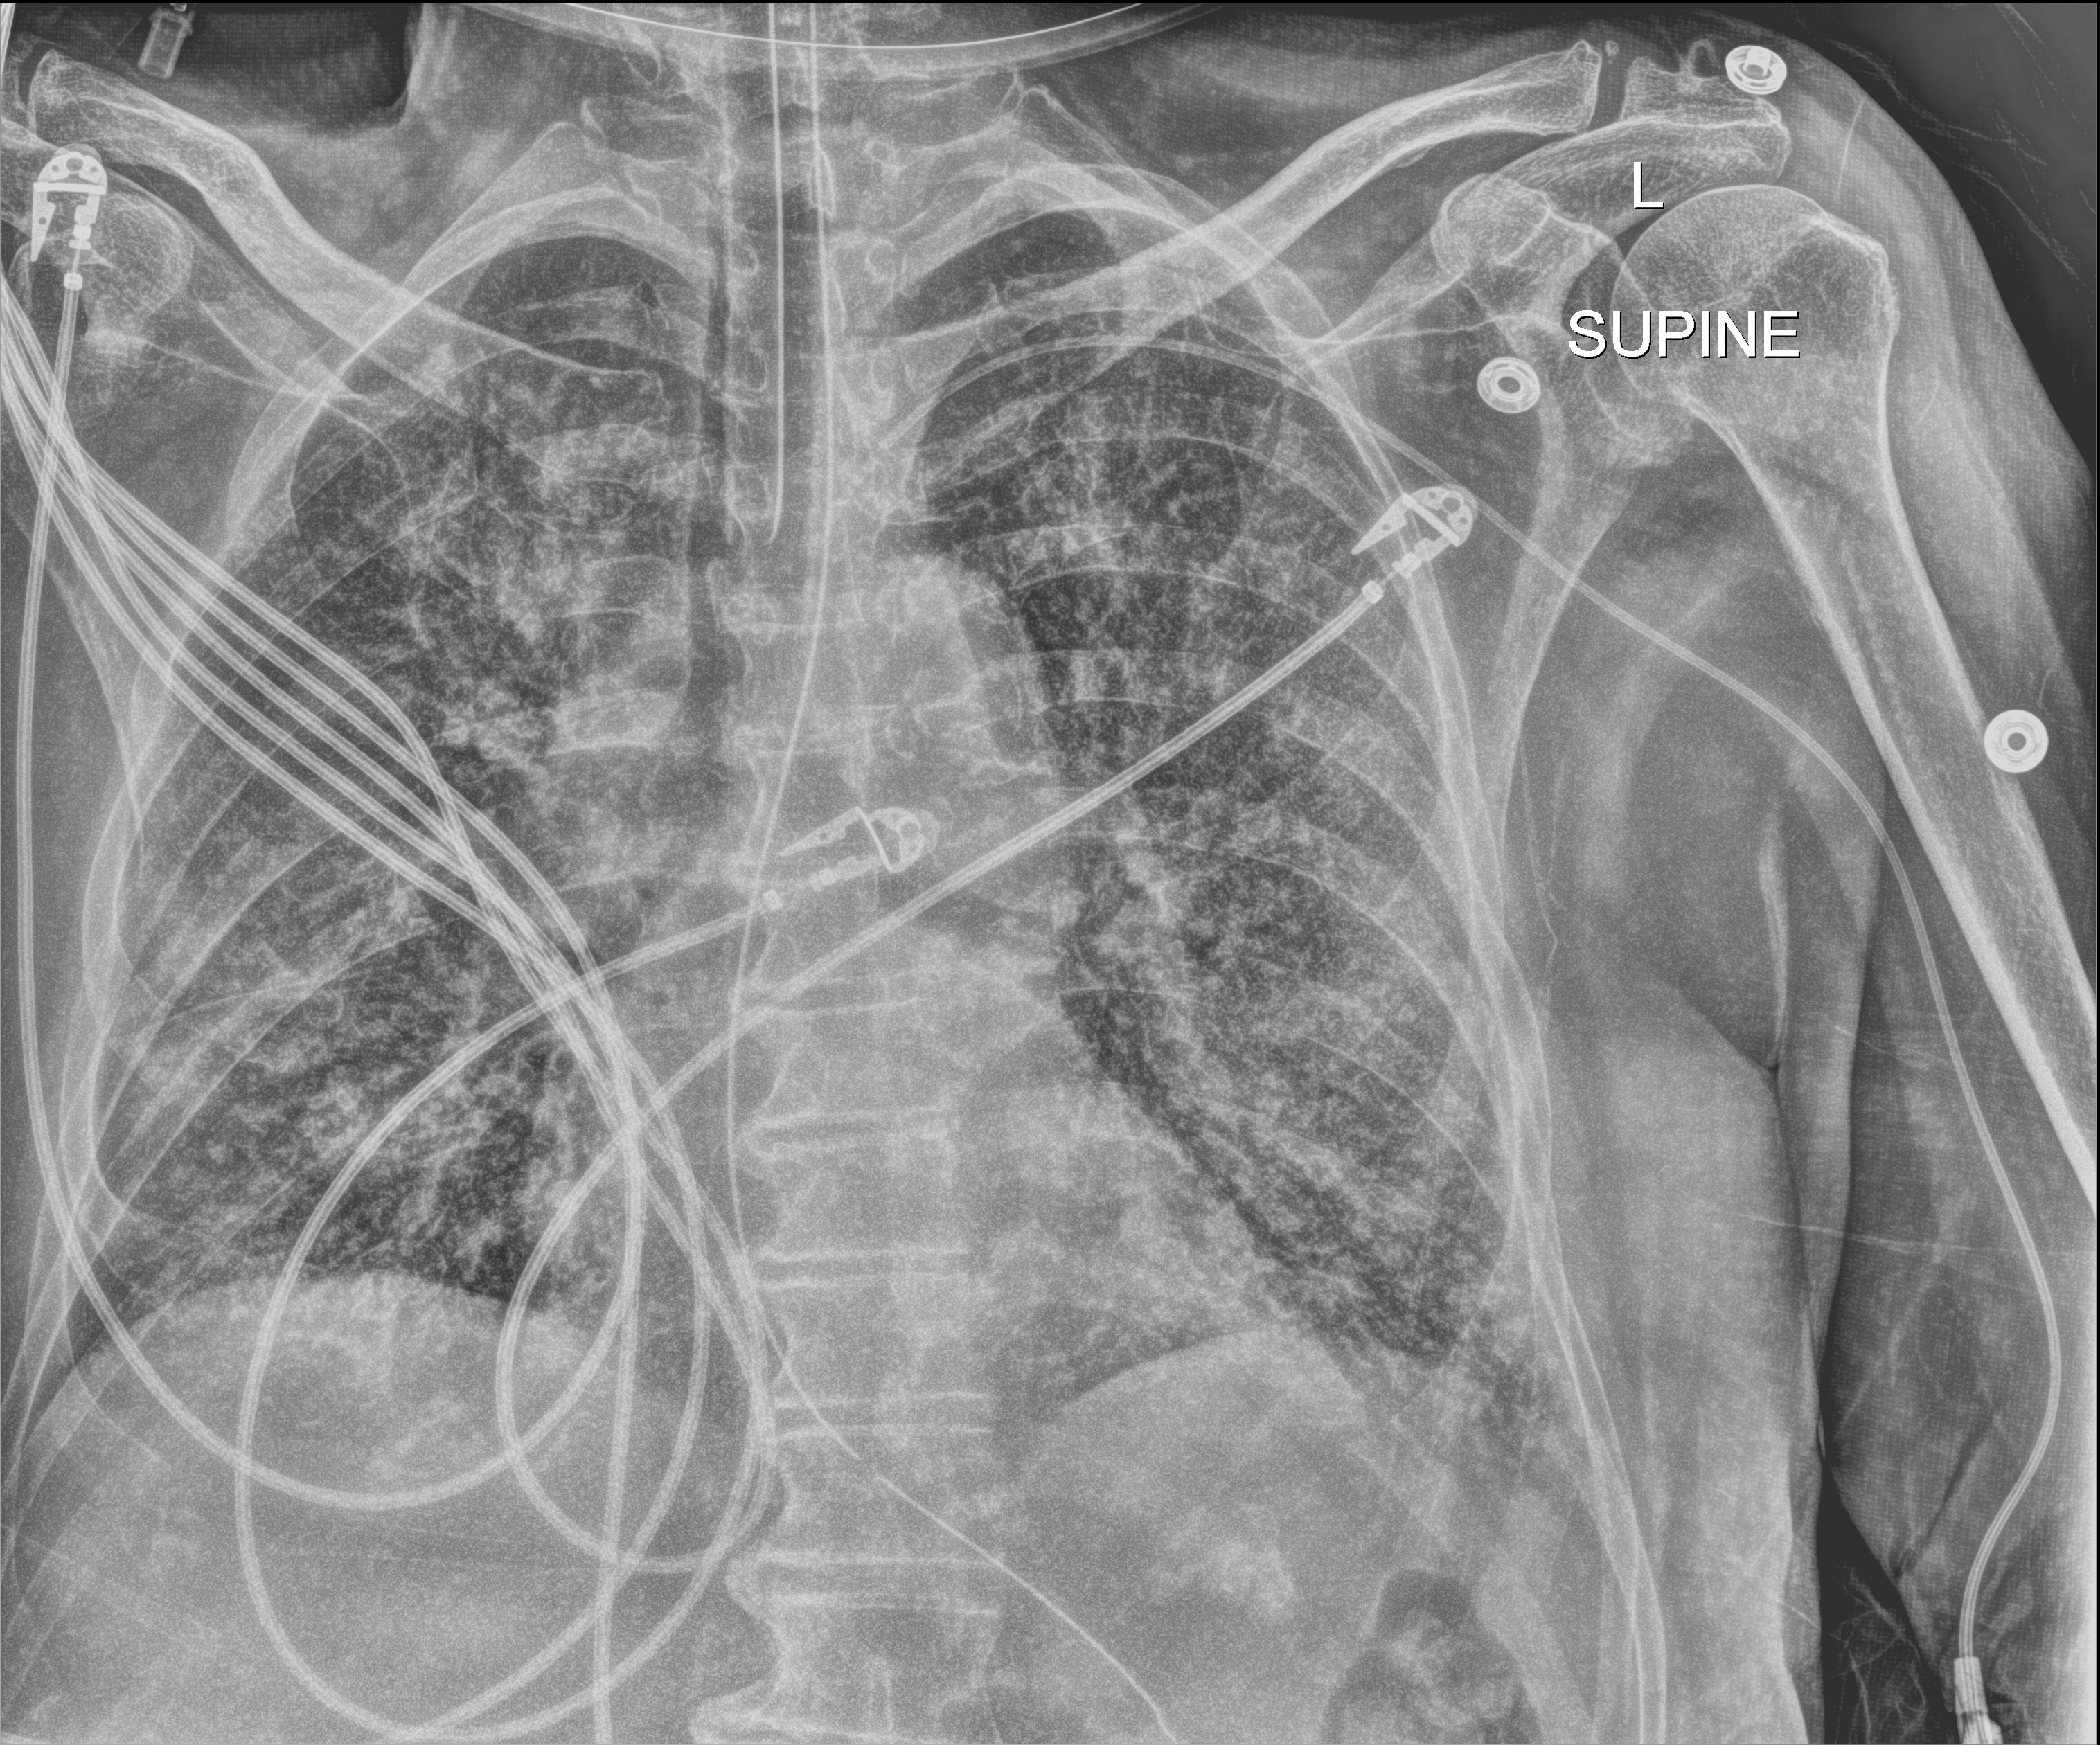
Portable chest radiograph, anteroposterior (AP) projection. Male patient hospitalised with COVID-19, age 75–90 years.
Hospital-stay facts (about this admission, not read from this image; timing relative to this image not recorded):
- mechanically ventilated during this hospital stay: yes
- diabetes (admission record): no
- admitted to intensive care during this hospital stay: yes